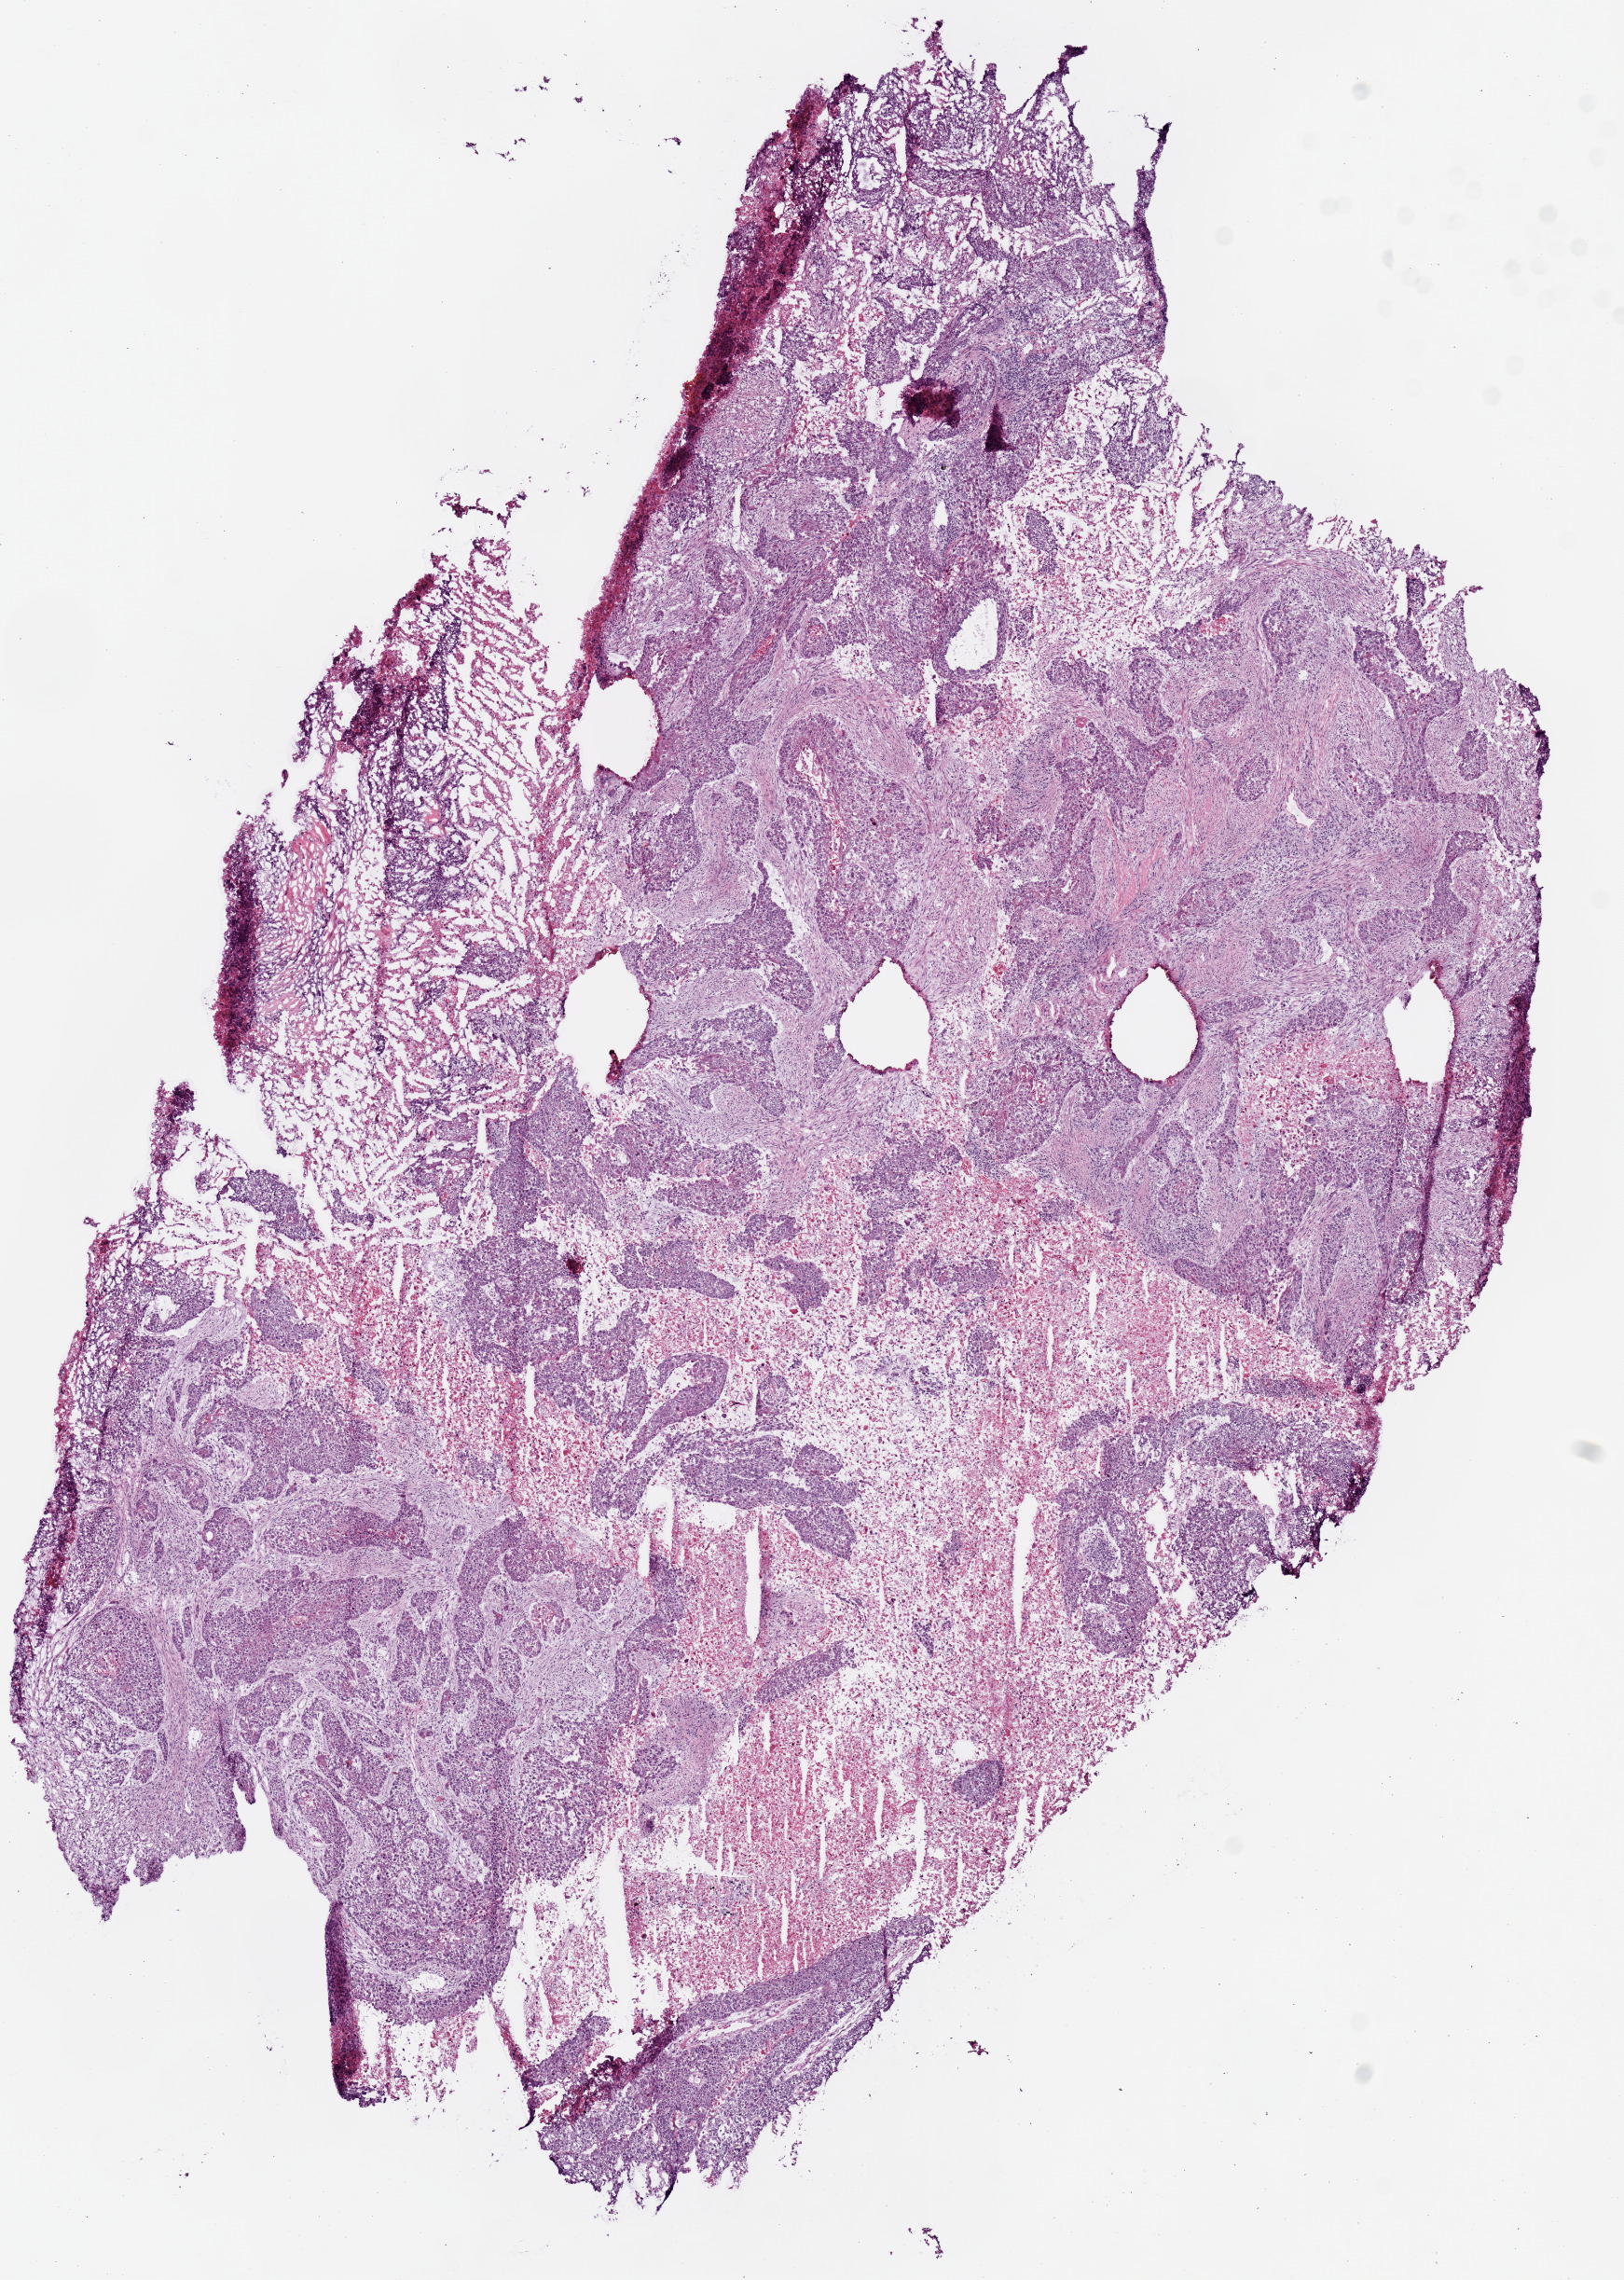
Digitized H&E tissue section (whole slide) — a low-resolution overview of the entire scanned area, about 6.9 x 9.7 mm. Frozen section. Lung, primary tumour sample. Patient: female, age at initial diagnosis 69 years. Pathologist review of this section (percent, as recorded): tumour cells 80%, tumour nuclei 60%, normal cells 0%, stromal cells 15%, necrosis 5%.
AJCC pathologic stage: IIB (6th edition). Diagnosis: Squamous cell carcinoma, NOS (upper lobe, lung).